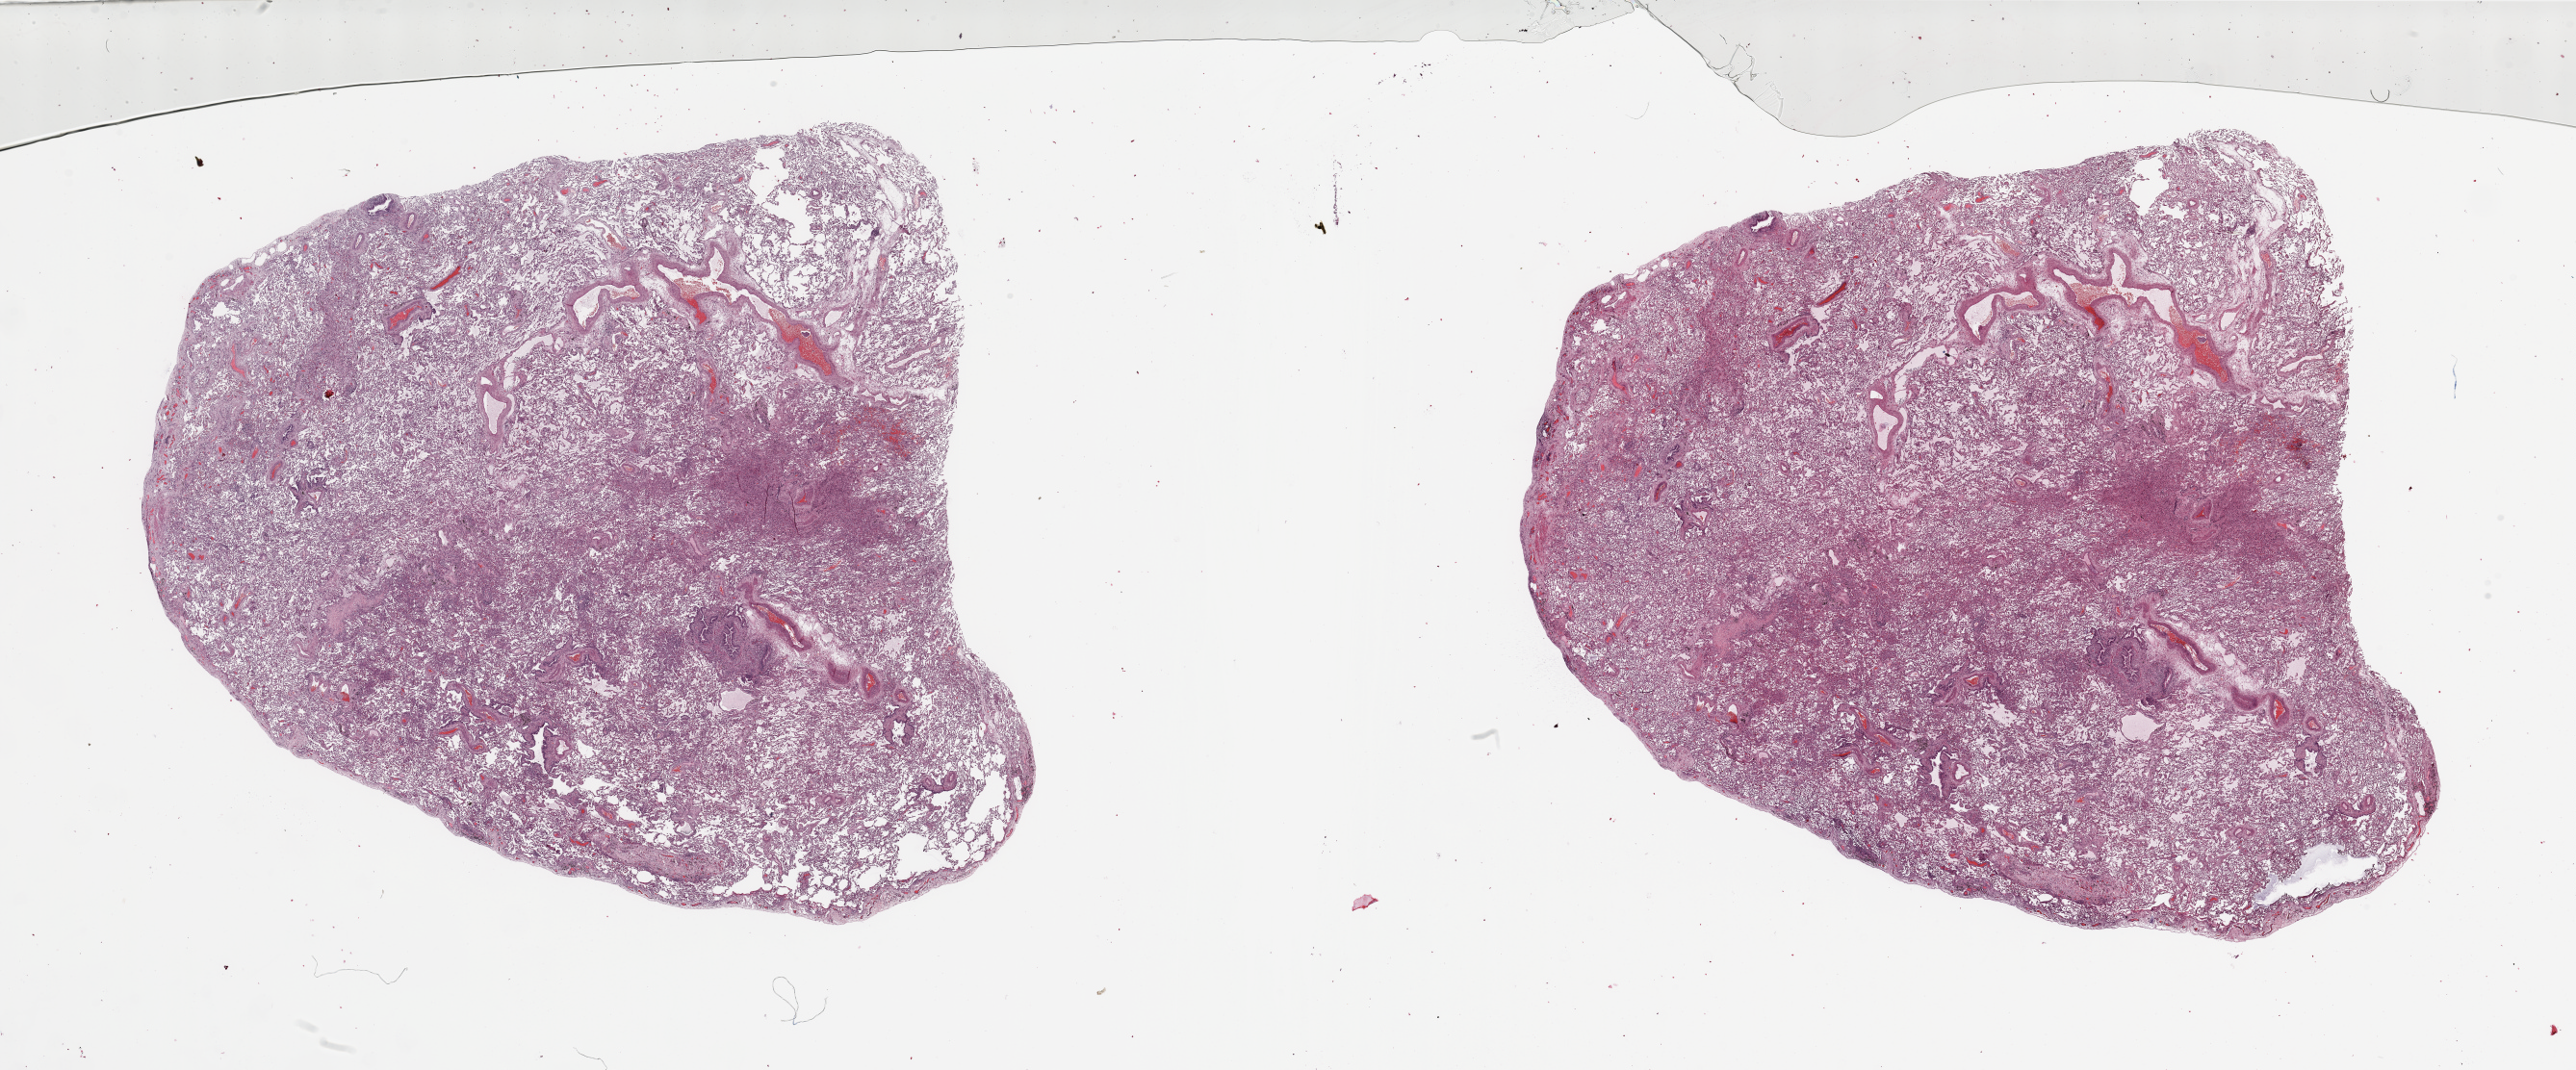
Hematoxylin and eosin (H&E) stained whole-slide image, shown as a low-resolution overview of the whole scanned area (about 42.3 x 17.6 mm), normal (non-tumour) tissue sample, sampled site: lung. Male, 74 y/o.
• this section: normal (non-tumour) tissue from the same patient
• patient diagnosis: Squamous cell carcinoma, NOS